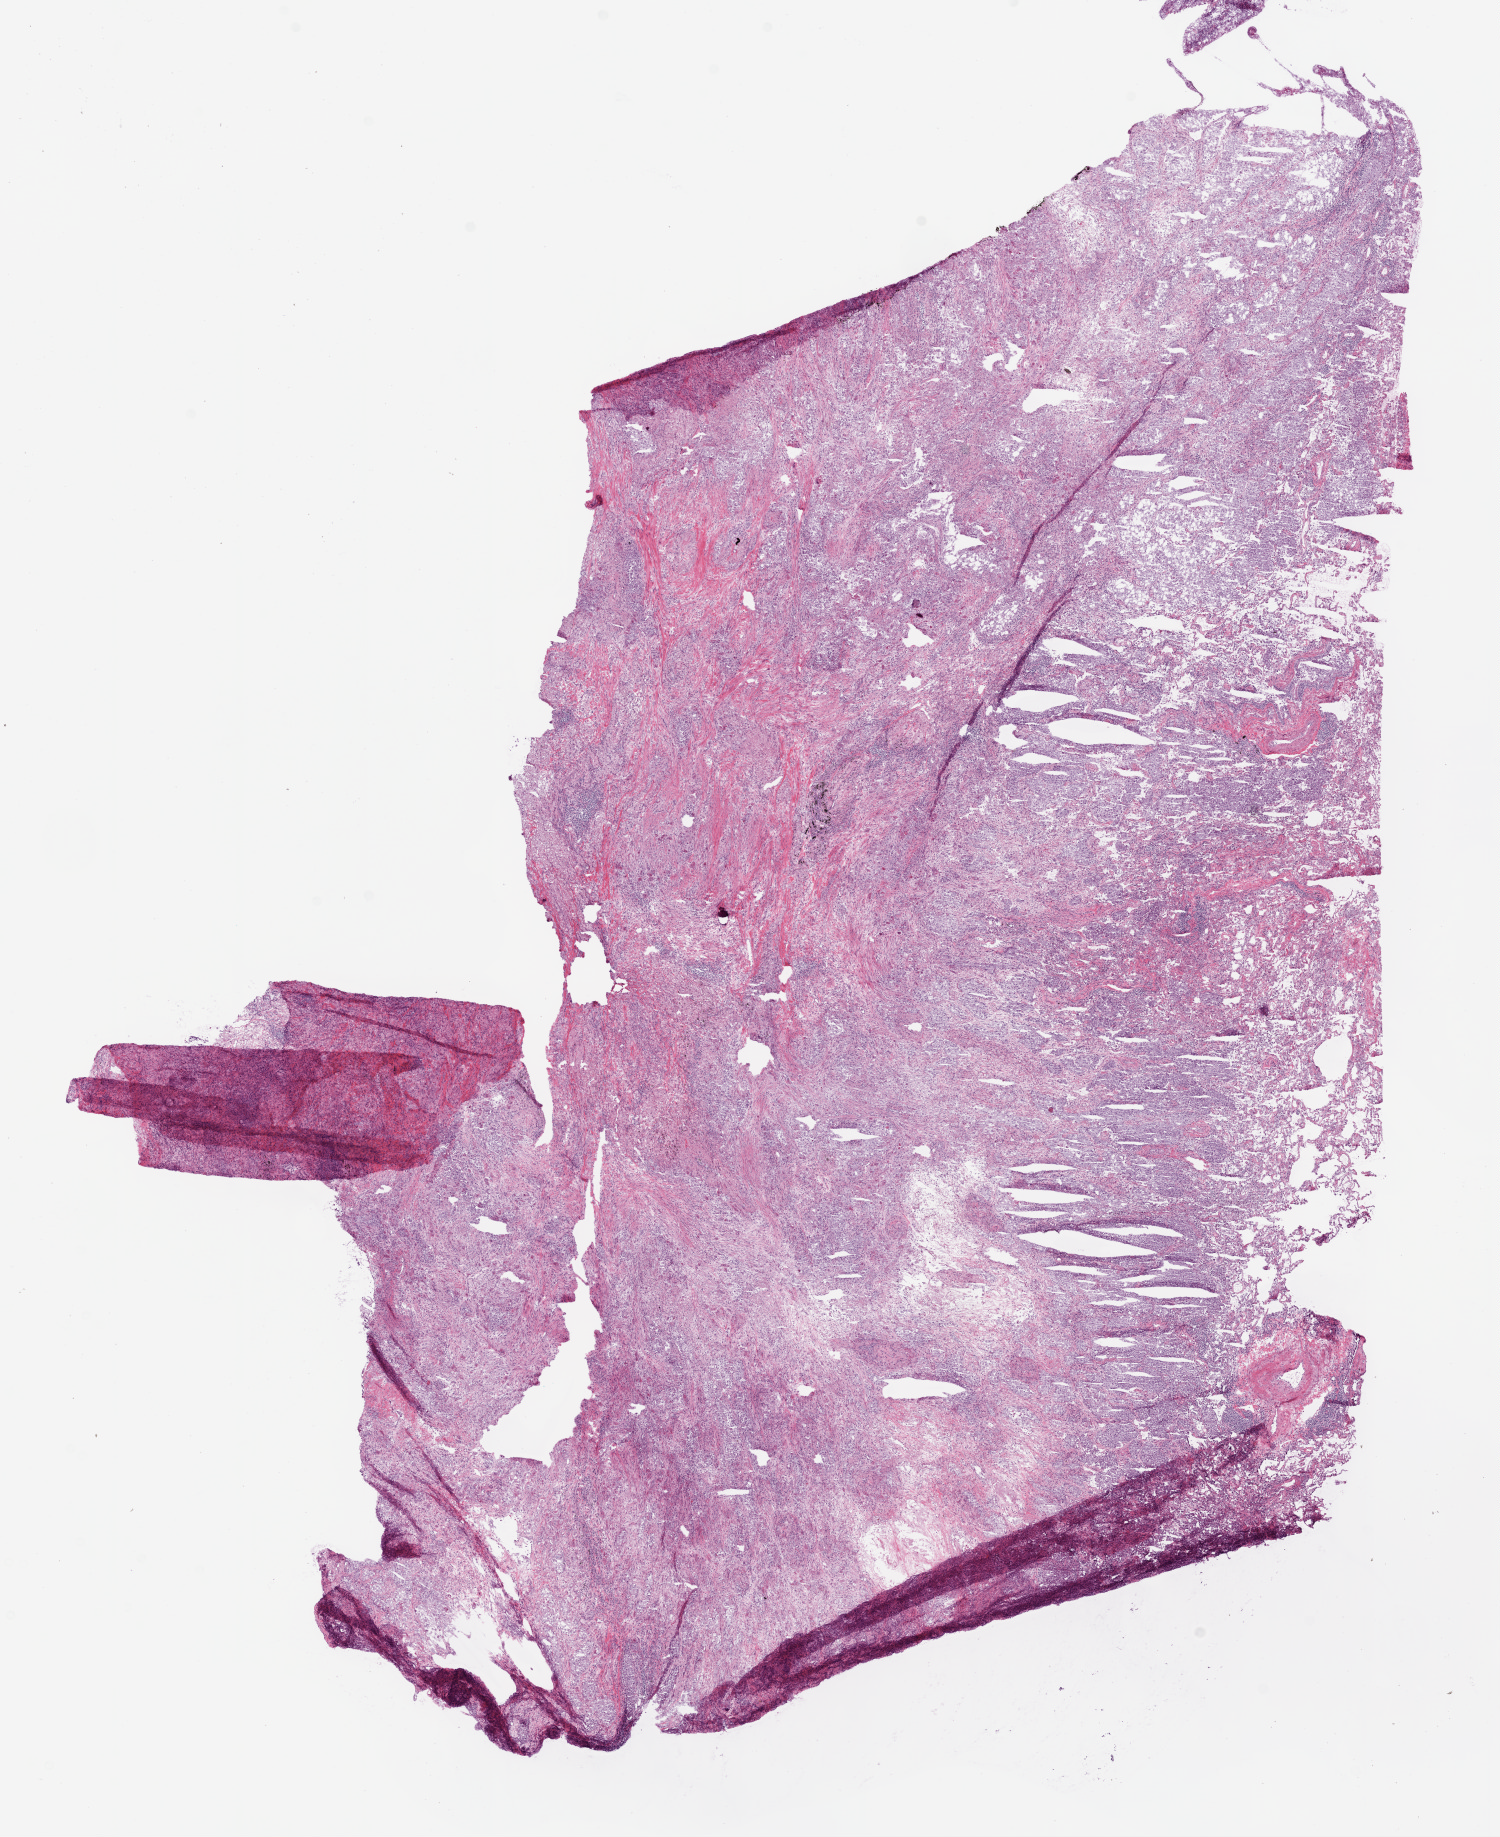
Whole-slide histology image, H&E-stained, whole scanned area (about 12.0 x 14.7 mm) shown as a low-resolution overview, frozen section, sample: primary tumour, lung. Female, age 77 years at initial diagnosis. Pathologist review of this section (percent, as recorded): tumour cells 45%, tumour nuclei 80%, normal cells 5%, stromal cells 30%, necrosis 20%.
Histologic diagnosis: Adenocarcinoma, NOS (lower lobe, lung). TNM: T1b N0 M0. AJCC pathologic stage: IA (6th edition).